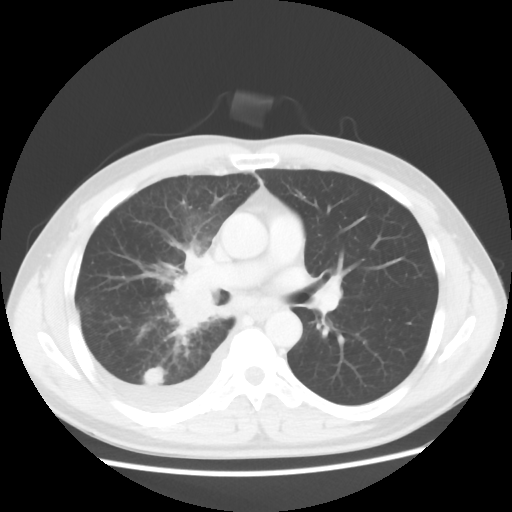
Chest CT, one axial slice; position 31 of 56 along the scan axis; reconstruction kernel STANDARD; 120 kVp; lung window (W 1500 / L -600 HU); 5 mm slice thickness; 512 × 512 image matrix, field of view 360 × 360 mm. Patient: male, 46 years. Case-level facts recorded for this patient, not image findings: clinical TNM (as recorded): T2 N3 M1.
Annotated regions visible in this slice (rectangle marked by the reading radiologist):
- lung tumour (recorded histology: adenocarcinoma): bounding box <161,268,217,330> (left, top, right, bottom; pixels)